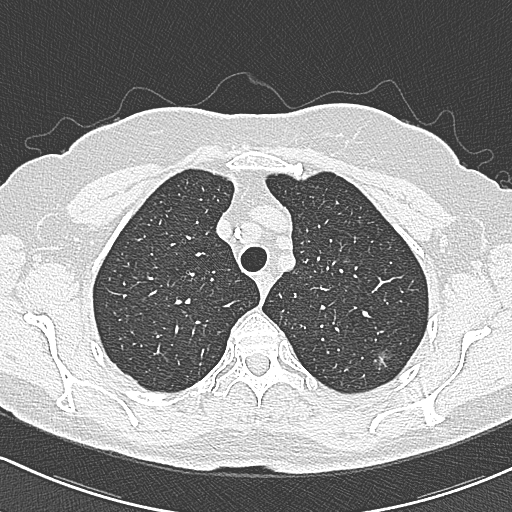
Chest CT (low-dose screening protocol), one axial image; baseline annual screen; lung window (W 1500 / L -600 HU); lung (sharp) reconstruction kernel (B80f); 120 kVp. Female participant, aged 65 years at enrolment. Current smoker at enrolment.
- Expert reader's lesion annotation, bounding box [x1, y1, x2, y2] px = [368, 345, 403, 380].
- The screening reader recorded 3 non-calcified nodules or masses ≥4 mm on this exam; which of them this box marks is not recorded.
- Lung cancer was diagnosed 390 days after this screen (after the second annual screen): bronchiolo-alveolar carcinoma, non-mucinous, left upper lobe, stage IA (AJCC 6th edition), 10 mm at pathology.